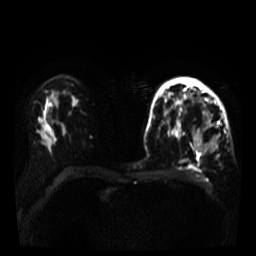
Breast MRI, one axial slice; slice 21 of 35 in the series (ordered by position); diffusion-weighted series; image 2 of 4 stored at this slice position (different b-values; order by instance number); 3 T; 5 mm slice thickness; 256 × 256 image matrix, field of view 320 × 320 mm. Female patient.
Structures marked on this image (manually delineated by an expert):
- tumour on diffusion-weighted imaging: bounding box [x1, y1, x2, y2] px = [193, 130, 220, 153]